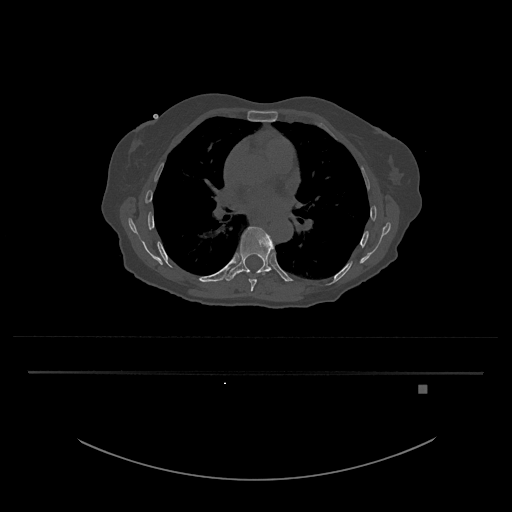
CT including the spine, one axial slice; slice 777 of 797 in the series (ordered by position); reconstruction kernel Br40s/3; bone window (W 1800 / L 400 HU); 0.5 mm slice thickness; 512 × 512 image matrix. Female patient, age 57 years. Case-level facts recorded for this patient, not image findings: primary cancer: cervical.
Structures marked on this image (semi-automatically segmented with operator editing):
- T8 vertebra: box from (x=242, y=271) to (x=265, y=292) px
- T9 vertebra: (x=225, y=227)–(x=274, y=281)